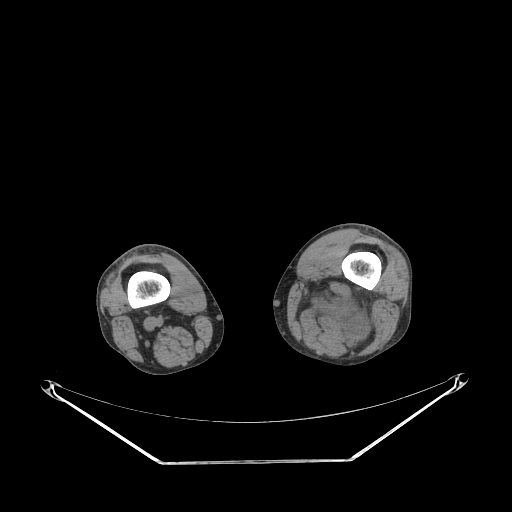
CT of an extremity soft-tissue mass (from a PET/CT study), one axial slice. Slice 203 of 267 in the series (ordered by position). Reconstruction kernel STANDARD. Soft-tissue window (W 400 / L 40 HU). 512 × 512 image matrix. Male patient. Case-level facts recorded for this patient, not image findings: histological type: undifferentiated pleomorphic liposarcoma; grade: high; site of the primary tumour: left thigh.
Annotated regions visible in this slice (expert contour drawn on MRI and transferred to this co-registered scan by the dataset authors):
- gross tumour volume including surrounding oedema: box from (x=295, y=278) to (x=380, y=352) px